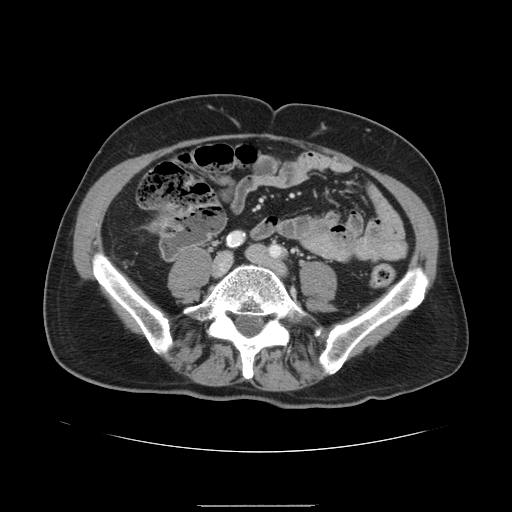
Contrast-enhanced abdominal CT, one axial slice; position 4 of 168 along the scan axis; intravenous contrast given; soft-tissue window (W 400 / L 40 HU); 2.5 mm slice thickness; 512 × 512 image matrix, field of view 386 × 386 mm. Male patient, age 74 years. From the clinical record (not read from this slice): diagnosis: colorectal cancer liver metastases, imaged before liver resection; multiple liver metastases: no; largest metastasis: 14.5 cm; disease in both lobes: yes.
Structures marked on this image (manually delineated by an expert):
- liver: bounding box <150,205,182,235> (left, top, right, bottom; pixels)